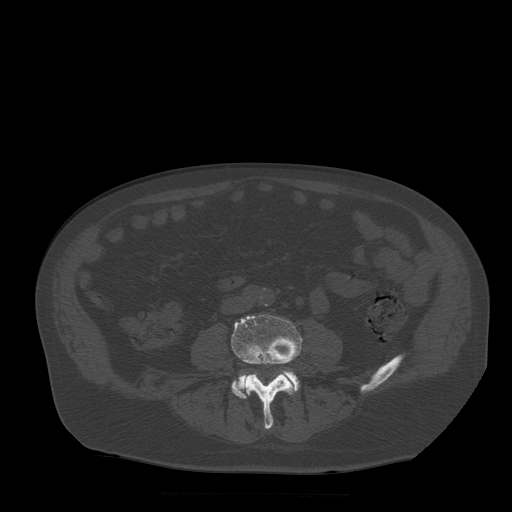
CT including the spine, one axial slice. Slice 109 of 522 in the series (ordered by position). Bone window (W 1800 / L 400 HU). 512 × 512 image matrix, field of view 420 × 420 mm. Patient age 72 years. Case-level facts recorded for this patient, not image findings: primary cancer: prostate.
Structures marked on this image (semi-automatic segmentation, software-assisted and operator-edited):
- L4 vertebra: bounding box <232,315,302,430> (left, top, right, bottom; pixels)
- L5 vertebra: <232,371,300,399>